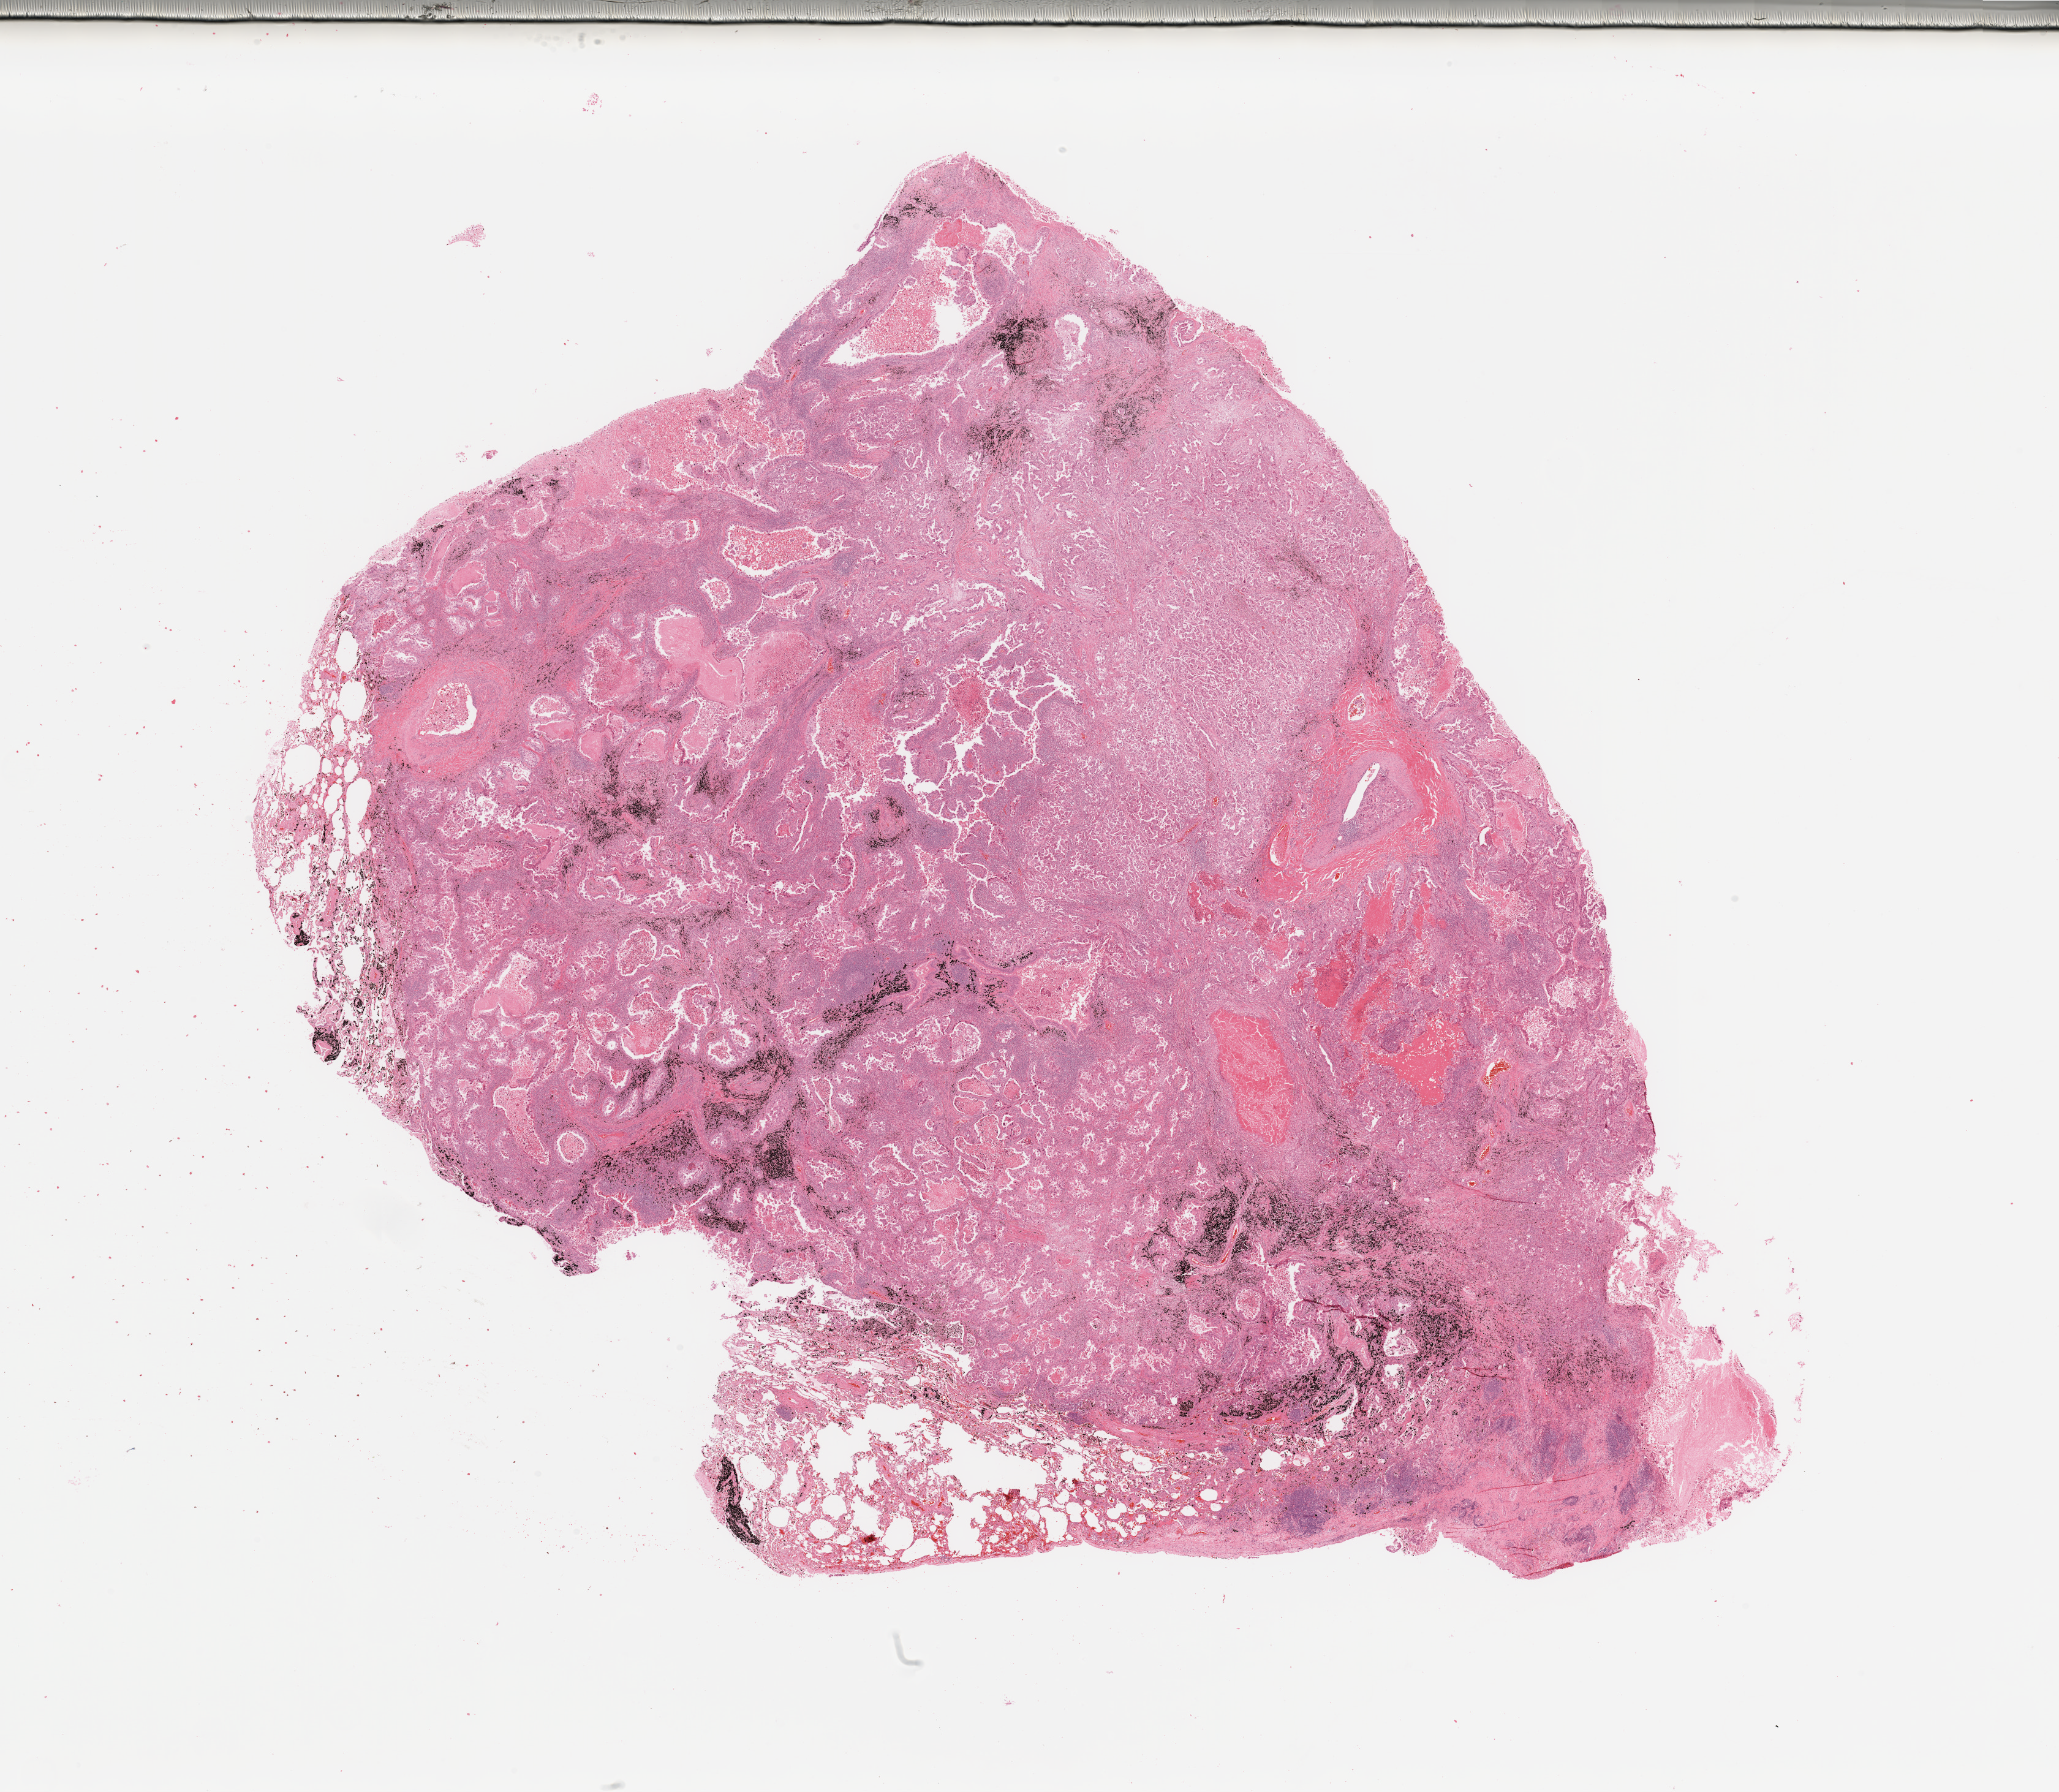
H&E whole-slide image — a low-resolution overview of the entire scanned area, about 26.6 x 23.1 mm (slide scanned at 20x). Tumour tissue sample, sampled site: lung. Male, 57 y/o. Histologic grade: G2 (moderately differentiated). Composition of this section per pathologist review: tumour nuclei 60%, necrosis 15%.
Histologic diagnosis: Adenocarcinoma, NOS. AJCC pathologic stage: IIIA.